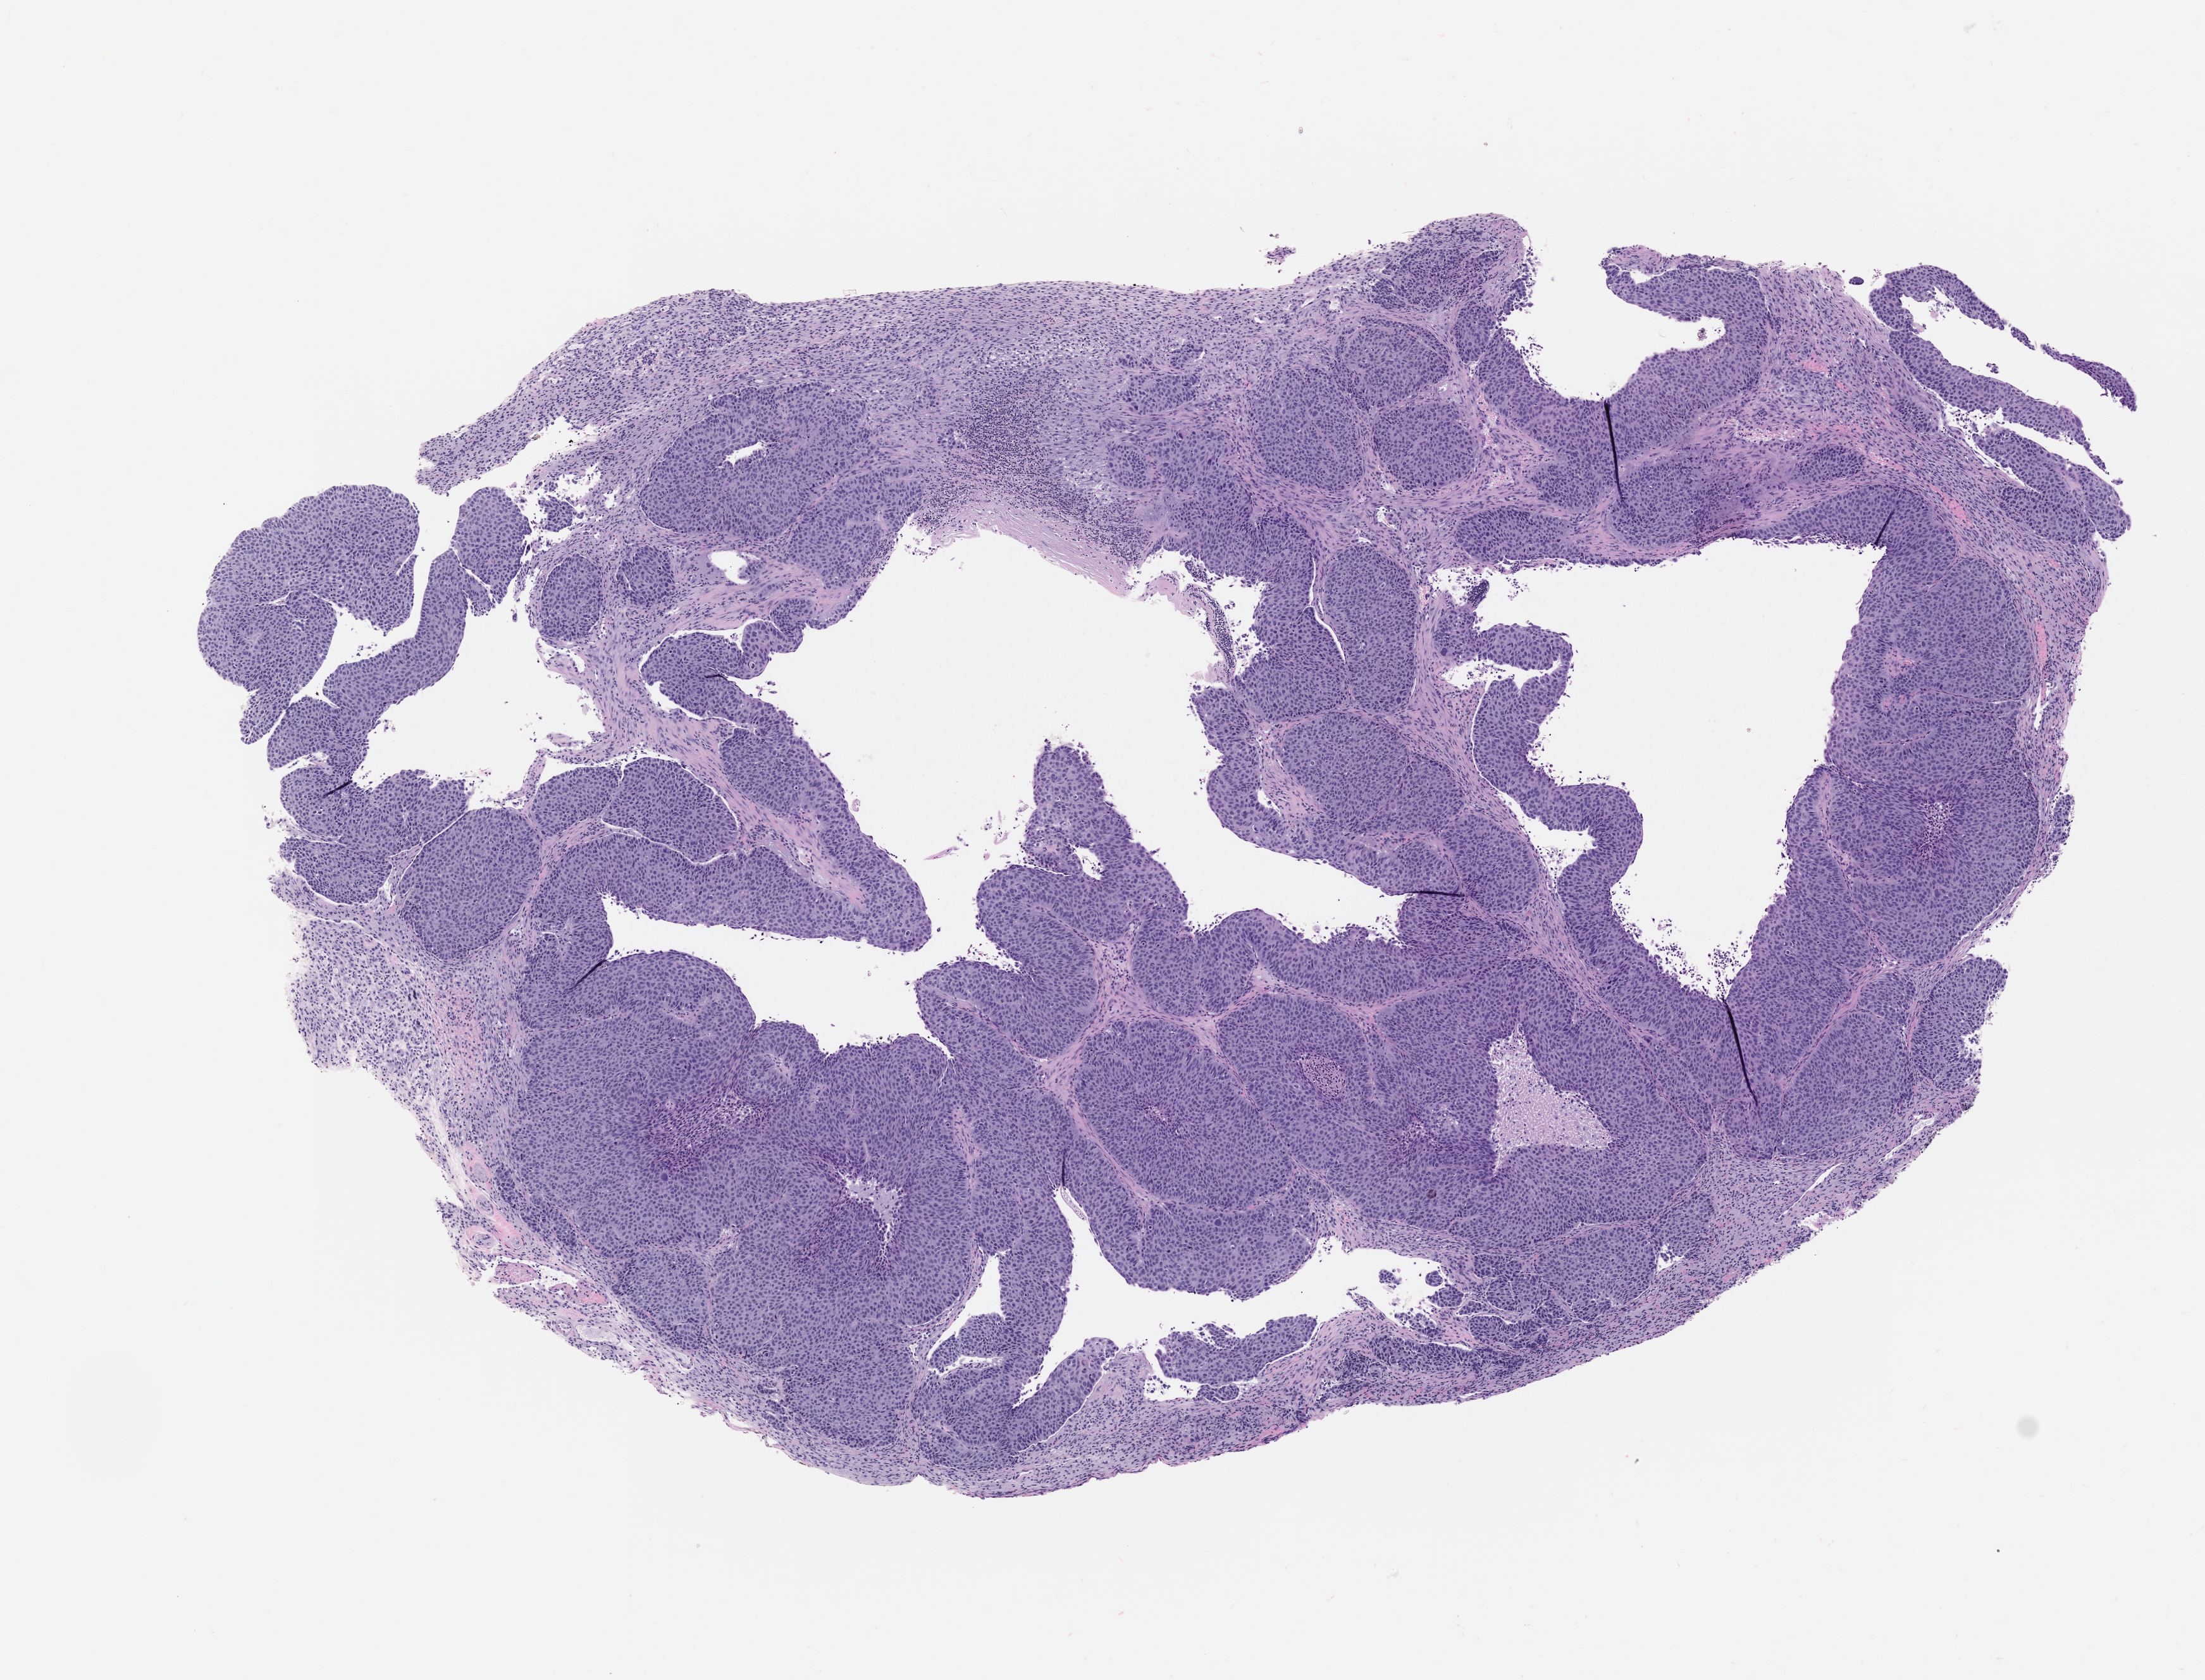
Whole-slide image, haematoxylin and eosin: patient-derived xenograft (human tumor grown in a mouse), passage 3, shown as a low-resolution overview of the whole scanned area (about 7.0 x 5.3 mm), FFPE section, originating tumor site category: lung.
Originating patient diagnosis: Lung Squamous Cell Carcinoma.